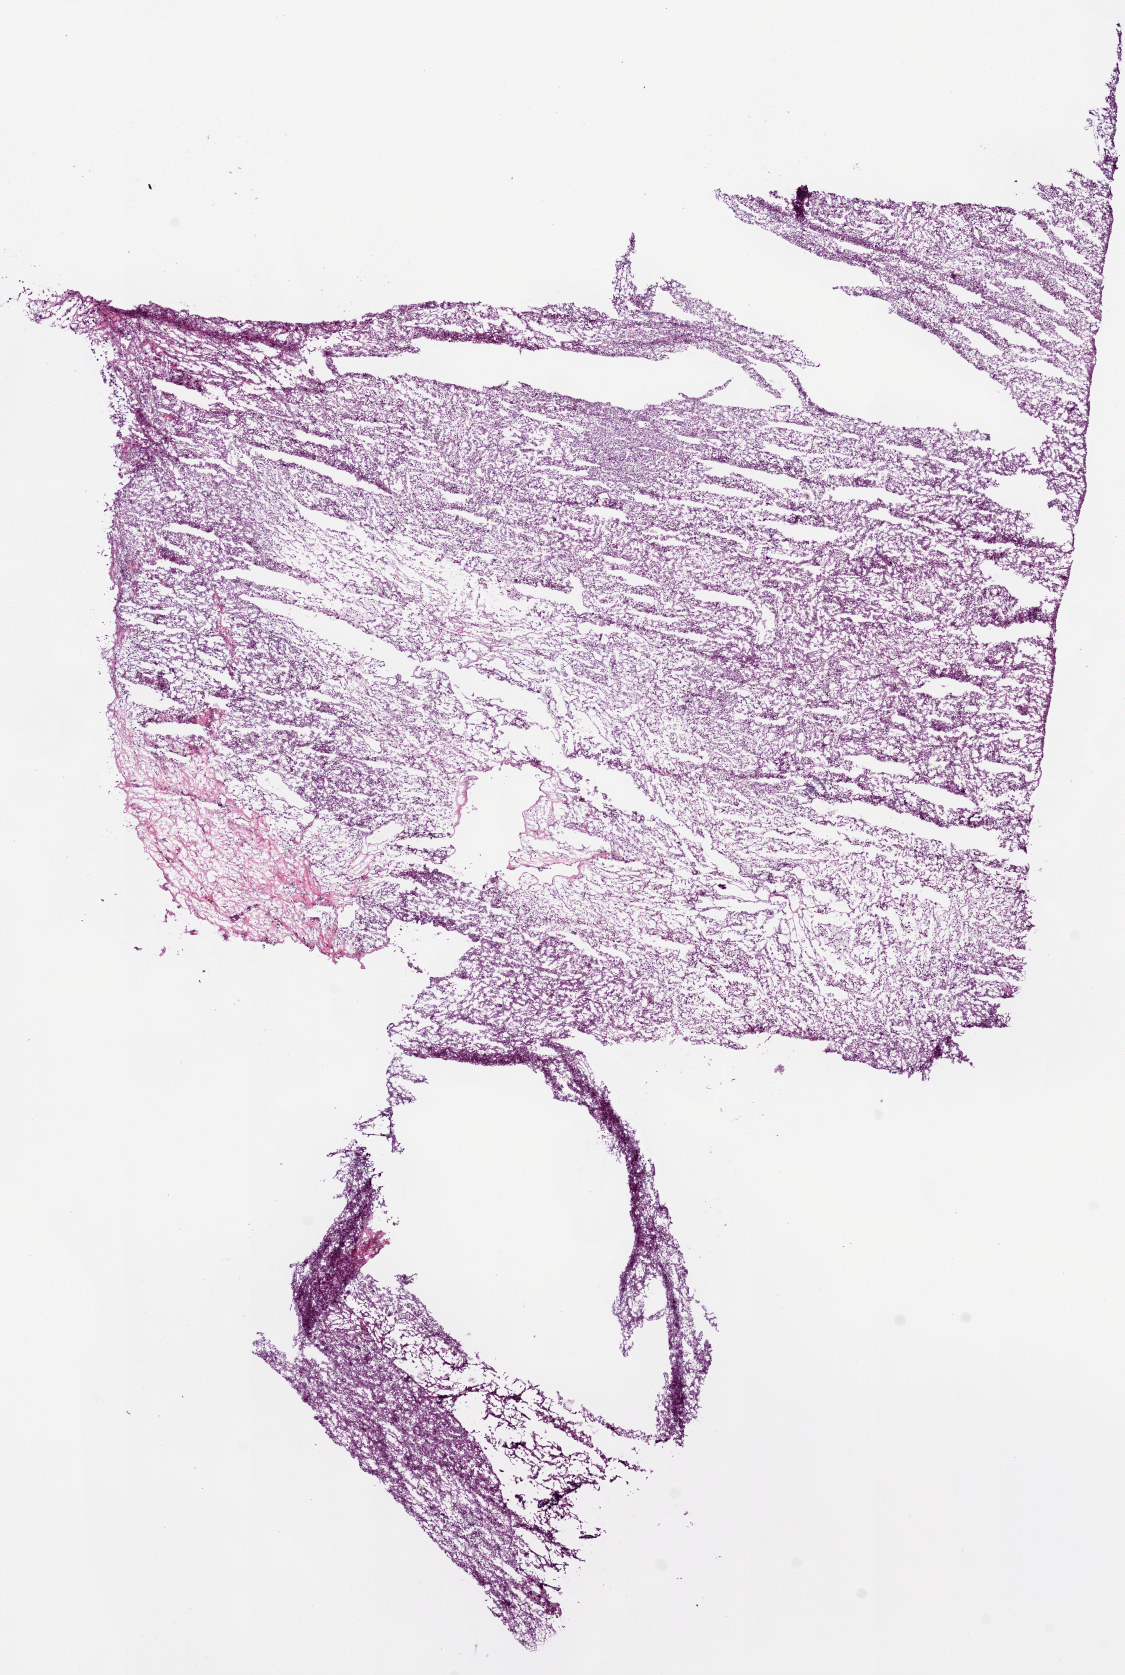
Hematoxylin and eosin (H&E) stained whole-slide image, low-resolution overview of the scanned area, about 9.0 x 13.4 mm (from a 20x scan). Frozen section from the bottom of the tissue portion. Kidney, primary tumour sample. Female, age 72 years at initial diagnosis. Histologic grade: G3 (poorly differentiated). Composition of this section per pathologist review: tumour cells 95%, tumour nuclei 90%, normal cells 0%, stromal cells 5%, necrosis 0%.
- diagnosis: Clear cell adenocarcinoma, NOS
- lymph nodes positive (case pathology): 0 of 2 examined
- AJCC pathologic stage: II